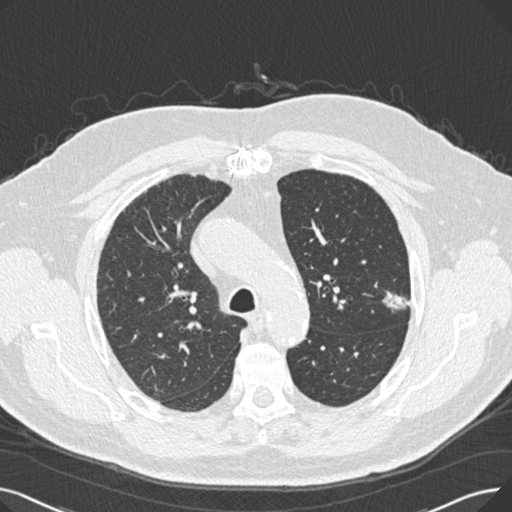
Low-dose screening chest CT, one axial slice. Position 189 of 269 along the scan axis. Reconstruction kernel B30f. 120 kVp. Lung window (W 1500 / L -600 HU). 512 × 512 image matrix, field of view 370 × 370 mm.
Annotated regions visible in this slice (outlined manually by an expert reader):
- lesion 1 (tumor, upper lobe of left lung): box from (x=382, y=291) to (x=411, y=312) px